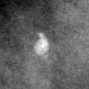
Region of interest cut from a scanned film mammogram (one marked finding); right breast; CC view.
Calcifications, morphology coarse; BI-RADS assessment category 2; benign without callback (not worked up further).